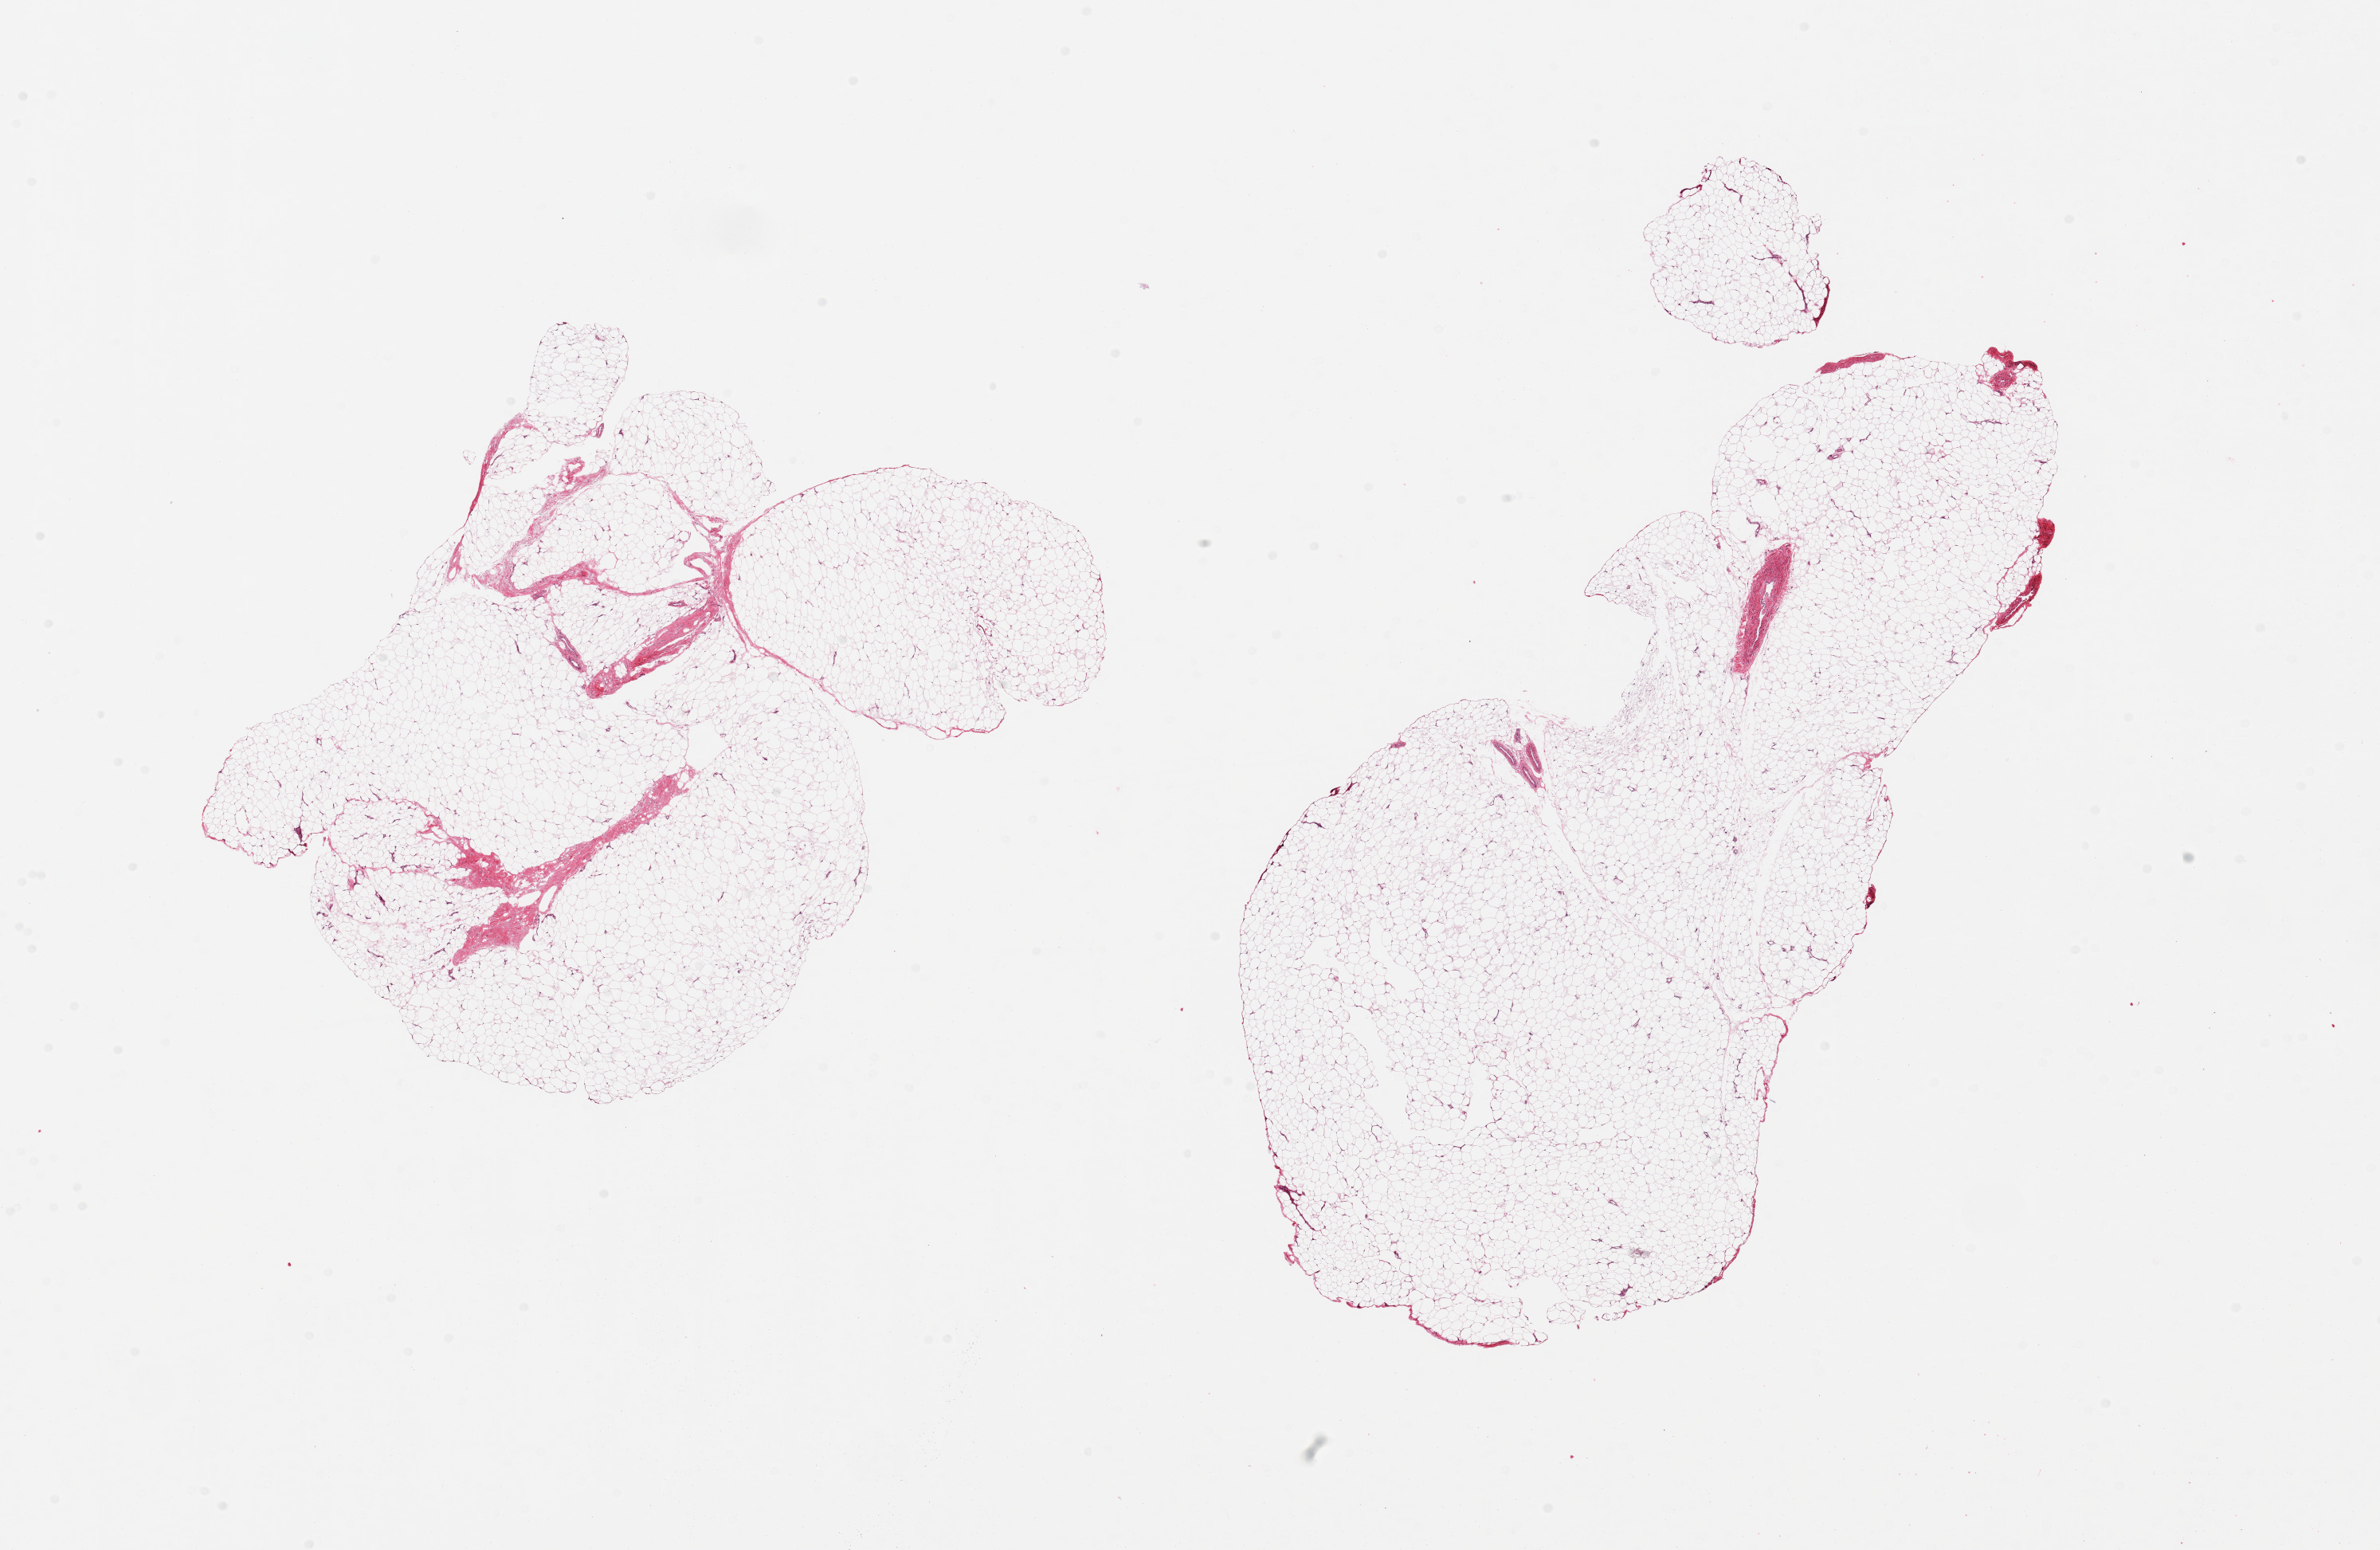
Digitized haematoxylin and eosin-stained section, low-resolution overview of the scanned area, about 23.6 x 15.4 mm; PAXgene-fixed paraffin-embedded (PFPE) section; sampled site (target tissue): adipose tissue; donor tissue sample. Female donor.
Pathologist's review note for this sample: 2 pieces; <5% fibrous content.